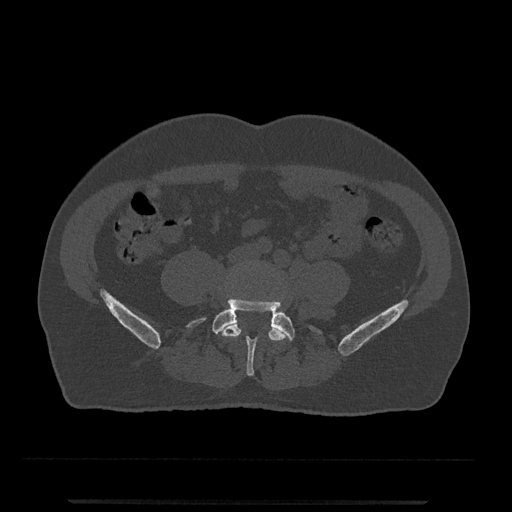
CT including the spine, one axial slice; position 94 of 797 along the scan axis; reconstruction kernel Br40s/3; 120 kVp; bone window (W 1800 / L 400 HU); 0.5 mm slice thickness; 512 × 512 image matrix, field of view 419 × 419 mm. Male patient, age 63 years. Case-level facts recorded for this patient, not image findings: primary cancer: prostate.
Annotated regions visible in this slice (semi-automatically segmented with operator editing):
- L4 vertebra: bounding box <222,320,289,363> (left, top, right, bottom; pixels)
- L5 vertebra: <187,299,321,376>